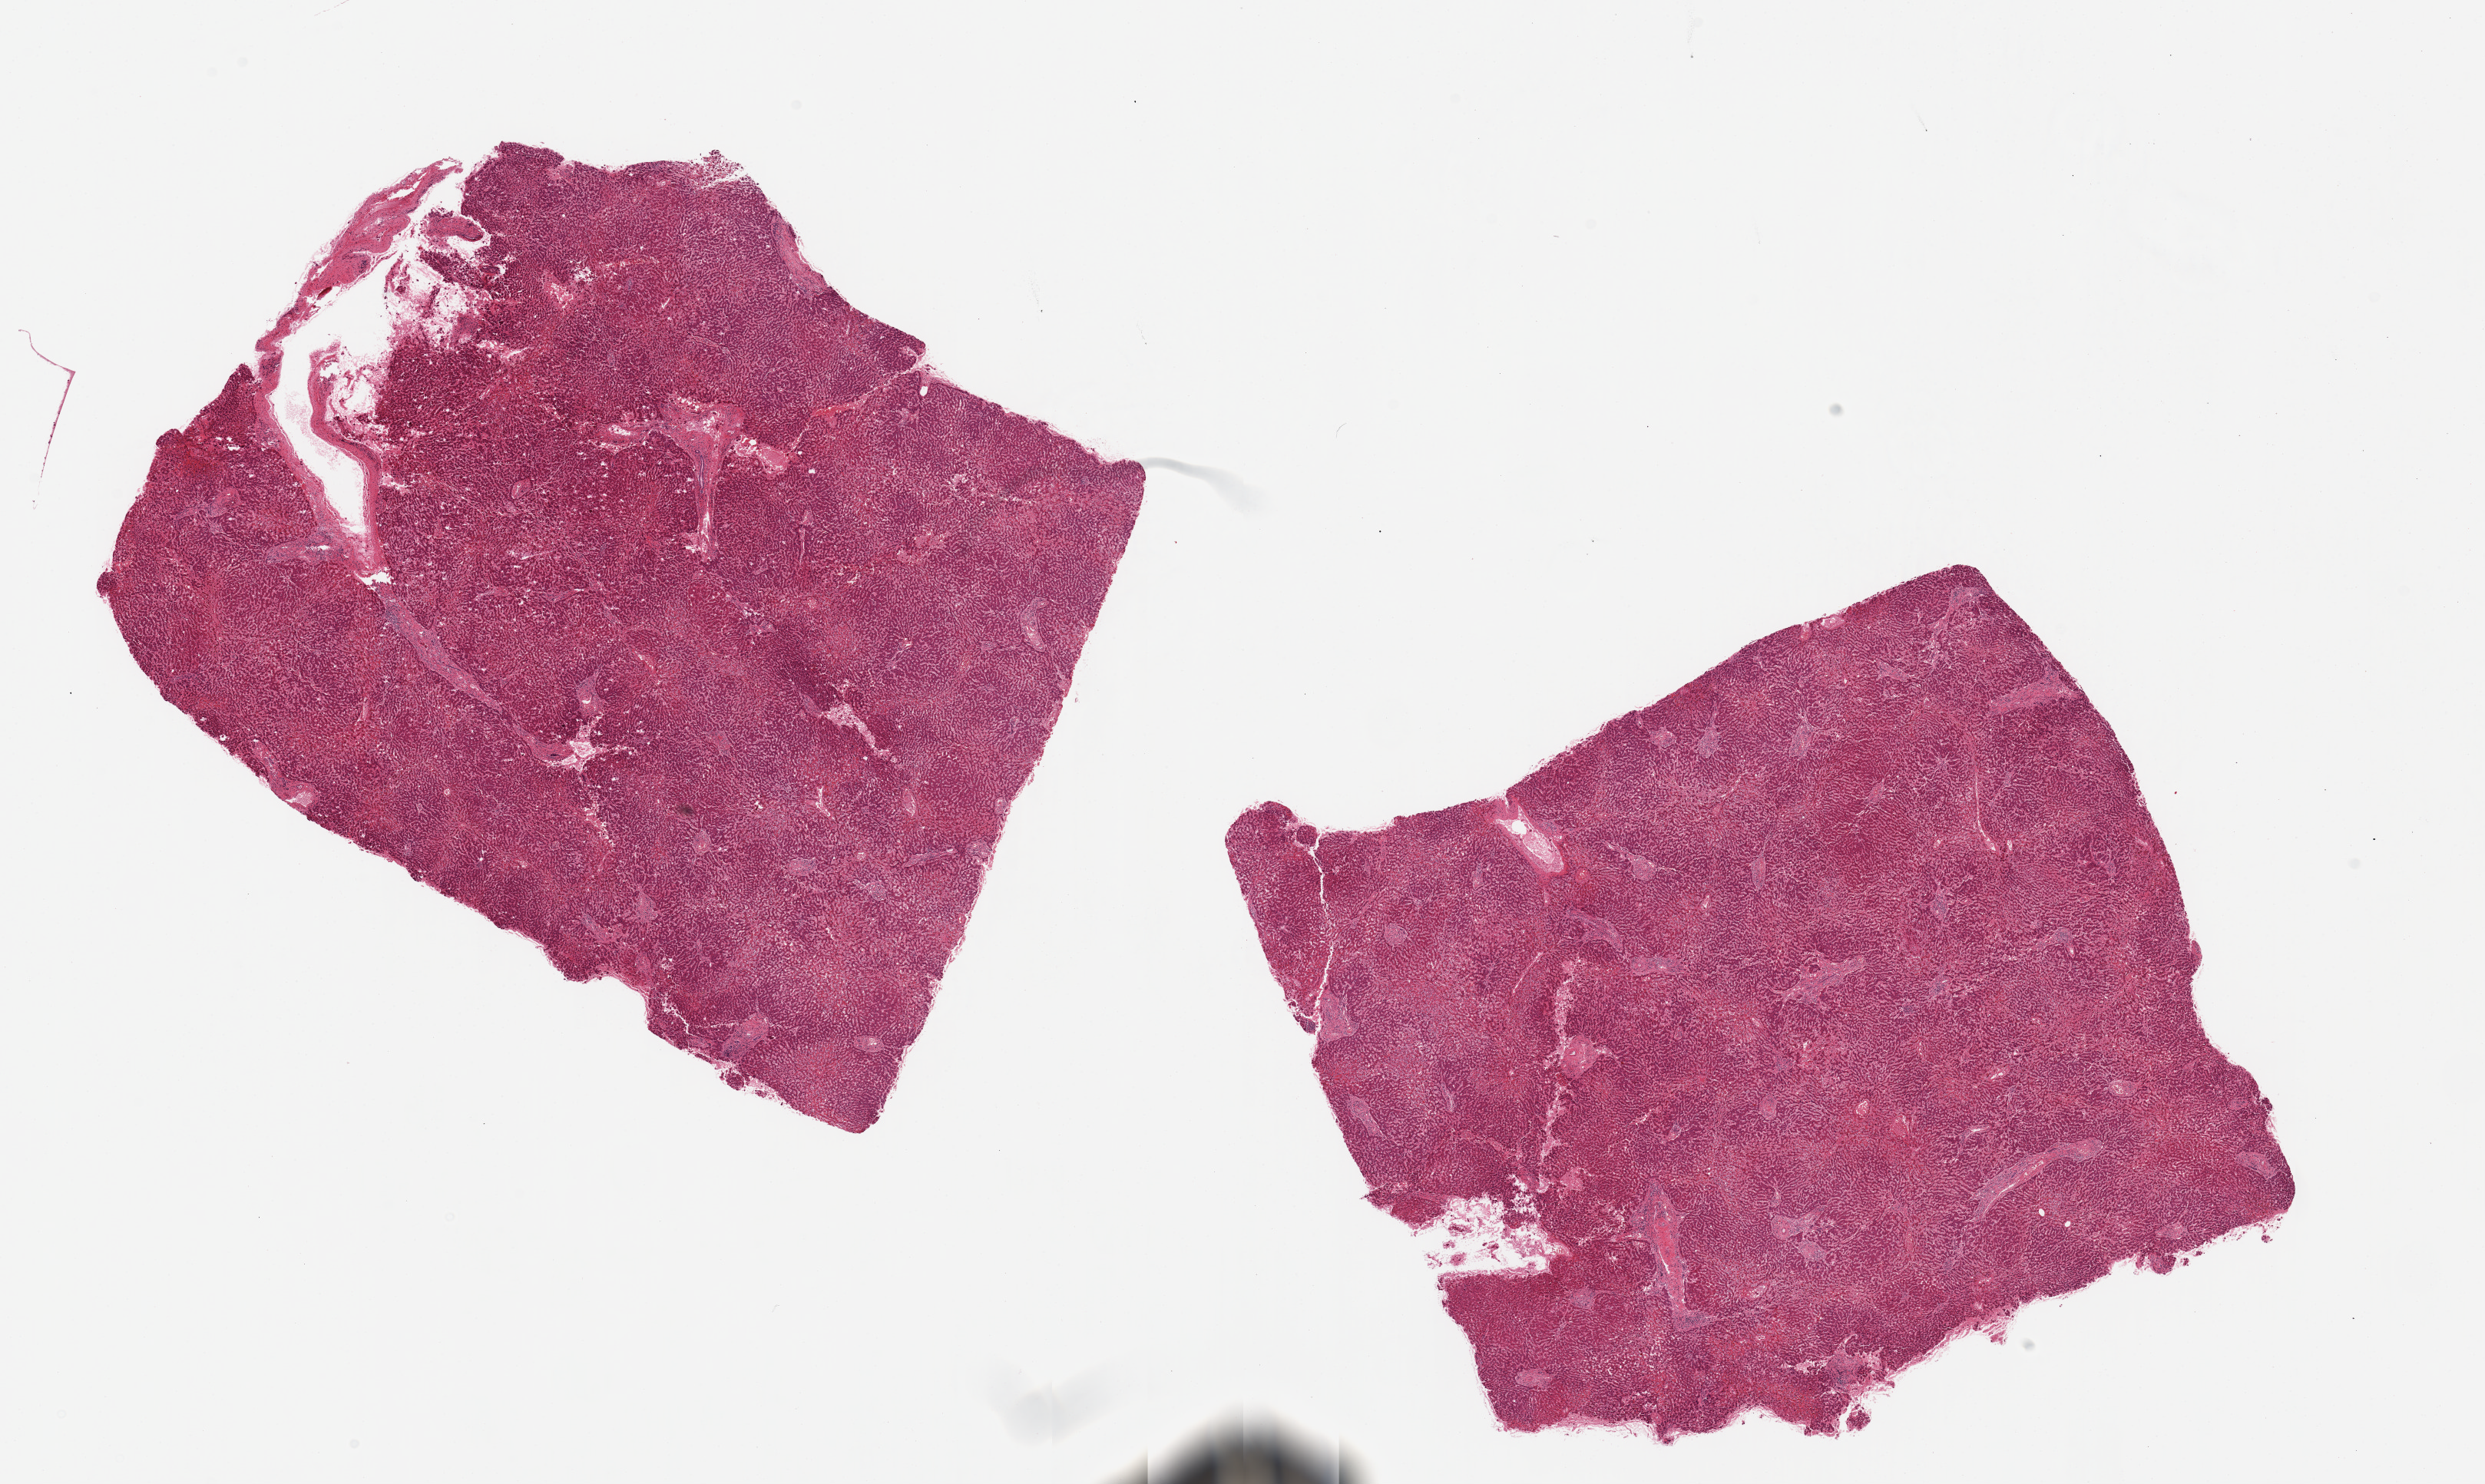
Whole-slide image, haematoxylin and eosin stain — low-resolution overview of the scanned area, about 25.6 x 15.3 mm. PAXgene-fixed, paraffin-embedded tissue. Section of liver (target tissue). Donor tissue sample. Donor sex: male.
Reviewer comment on this tissue sample: 2 pieces. Central congestion and degeneration.